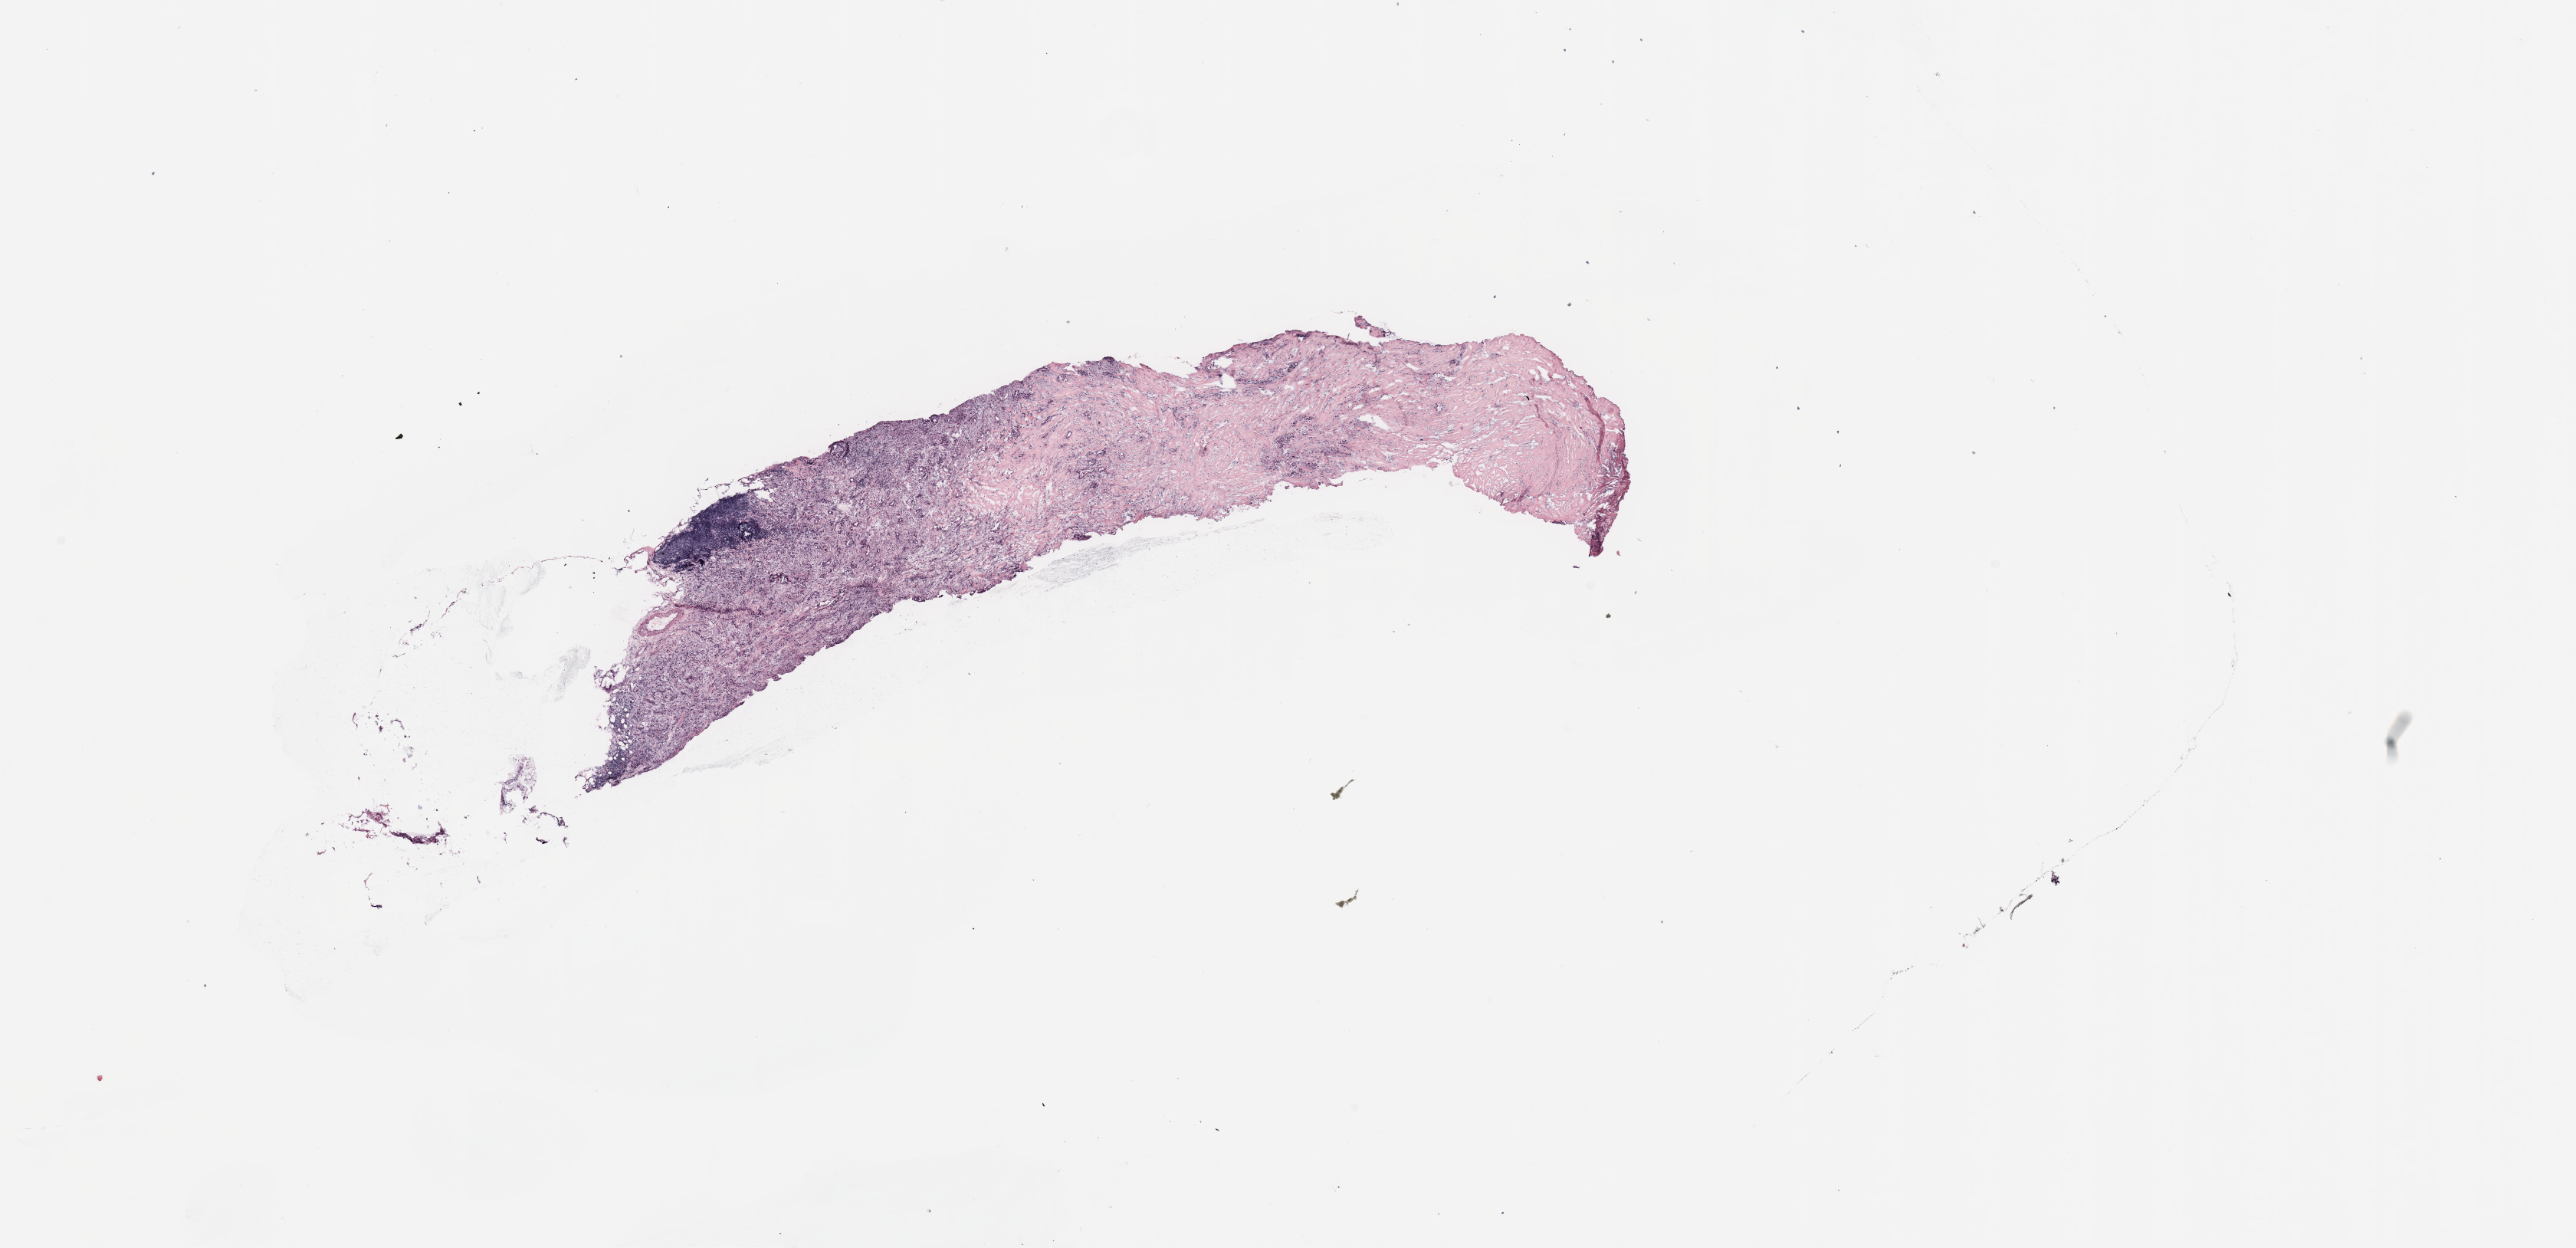
Whole-slide histology image, H&E — whole scanned area (about 26.6 x 12.9 mm) shown as a low-resolution overview. Female, 65 y/o.
Specimen: tumour tissue sample, breast.